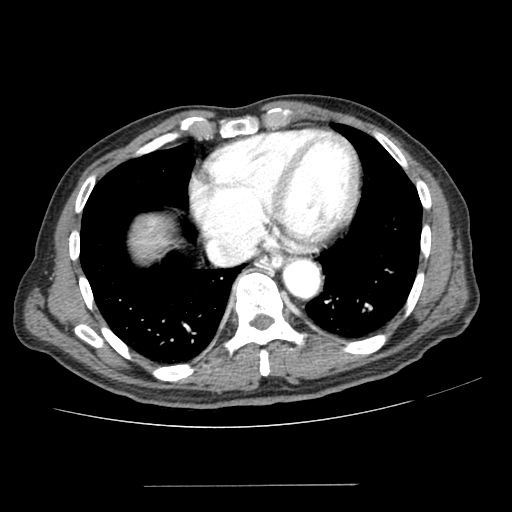
Contrast-enhanced abdominal CT (liver protocol), one axial slice. 100 kVp. Soft-tissue window (W 400 / L 40 HU). 512 × 512 image matrix, field of view 360 × 360 mm. From the clinical record (not read from this slice): diagnosis: hepatocellular carcinoma (patient treated with transarterial chemoembolisation; whether this scan precedes or follows treatment is not stated here); TNM stage (as recorded): Stage-I; Child-Pugh class: A; tumour differentiation: poorly differentiated; tumour nodularity: uninodular.
Annotated regions visible in this slice (semi-automatically segmented with operator editing):
- liver parenchyma outside the tumour (the mass and vessels are separate outlines, so this box may not span the whole liver): bounding box [x1, y1, x2, y2] px = [130, 214, 170, 258]